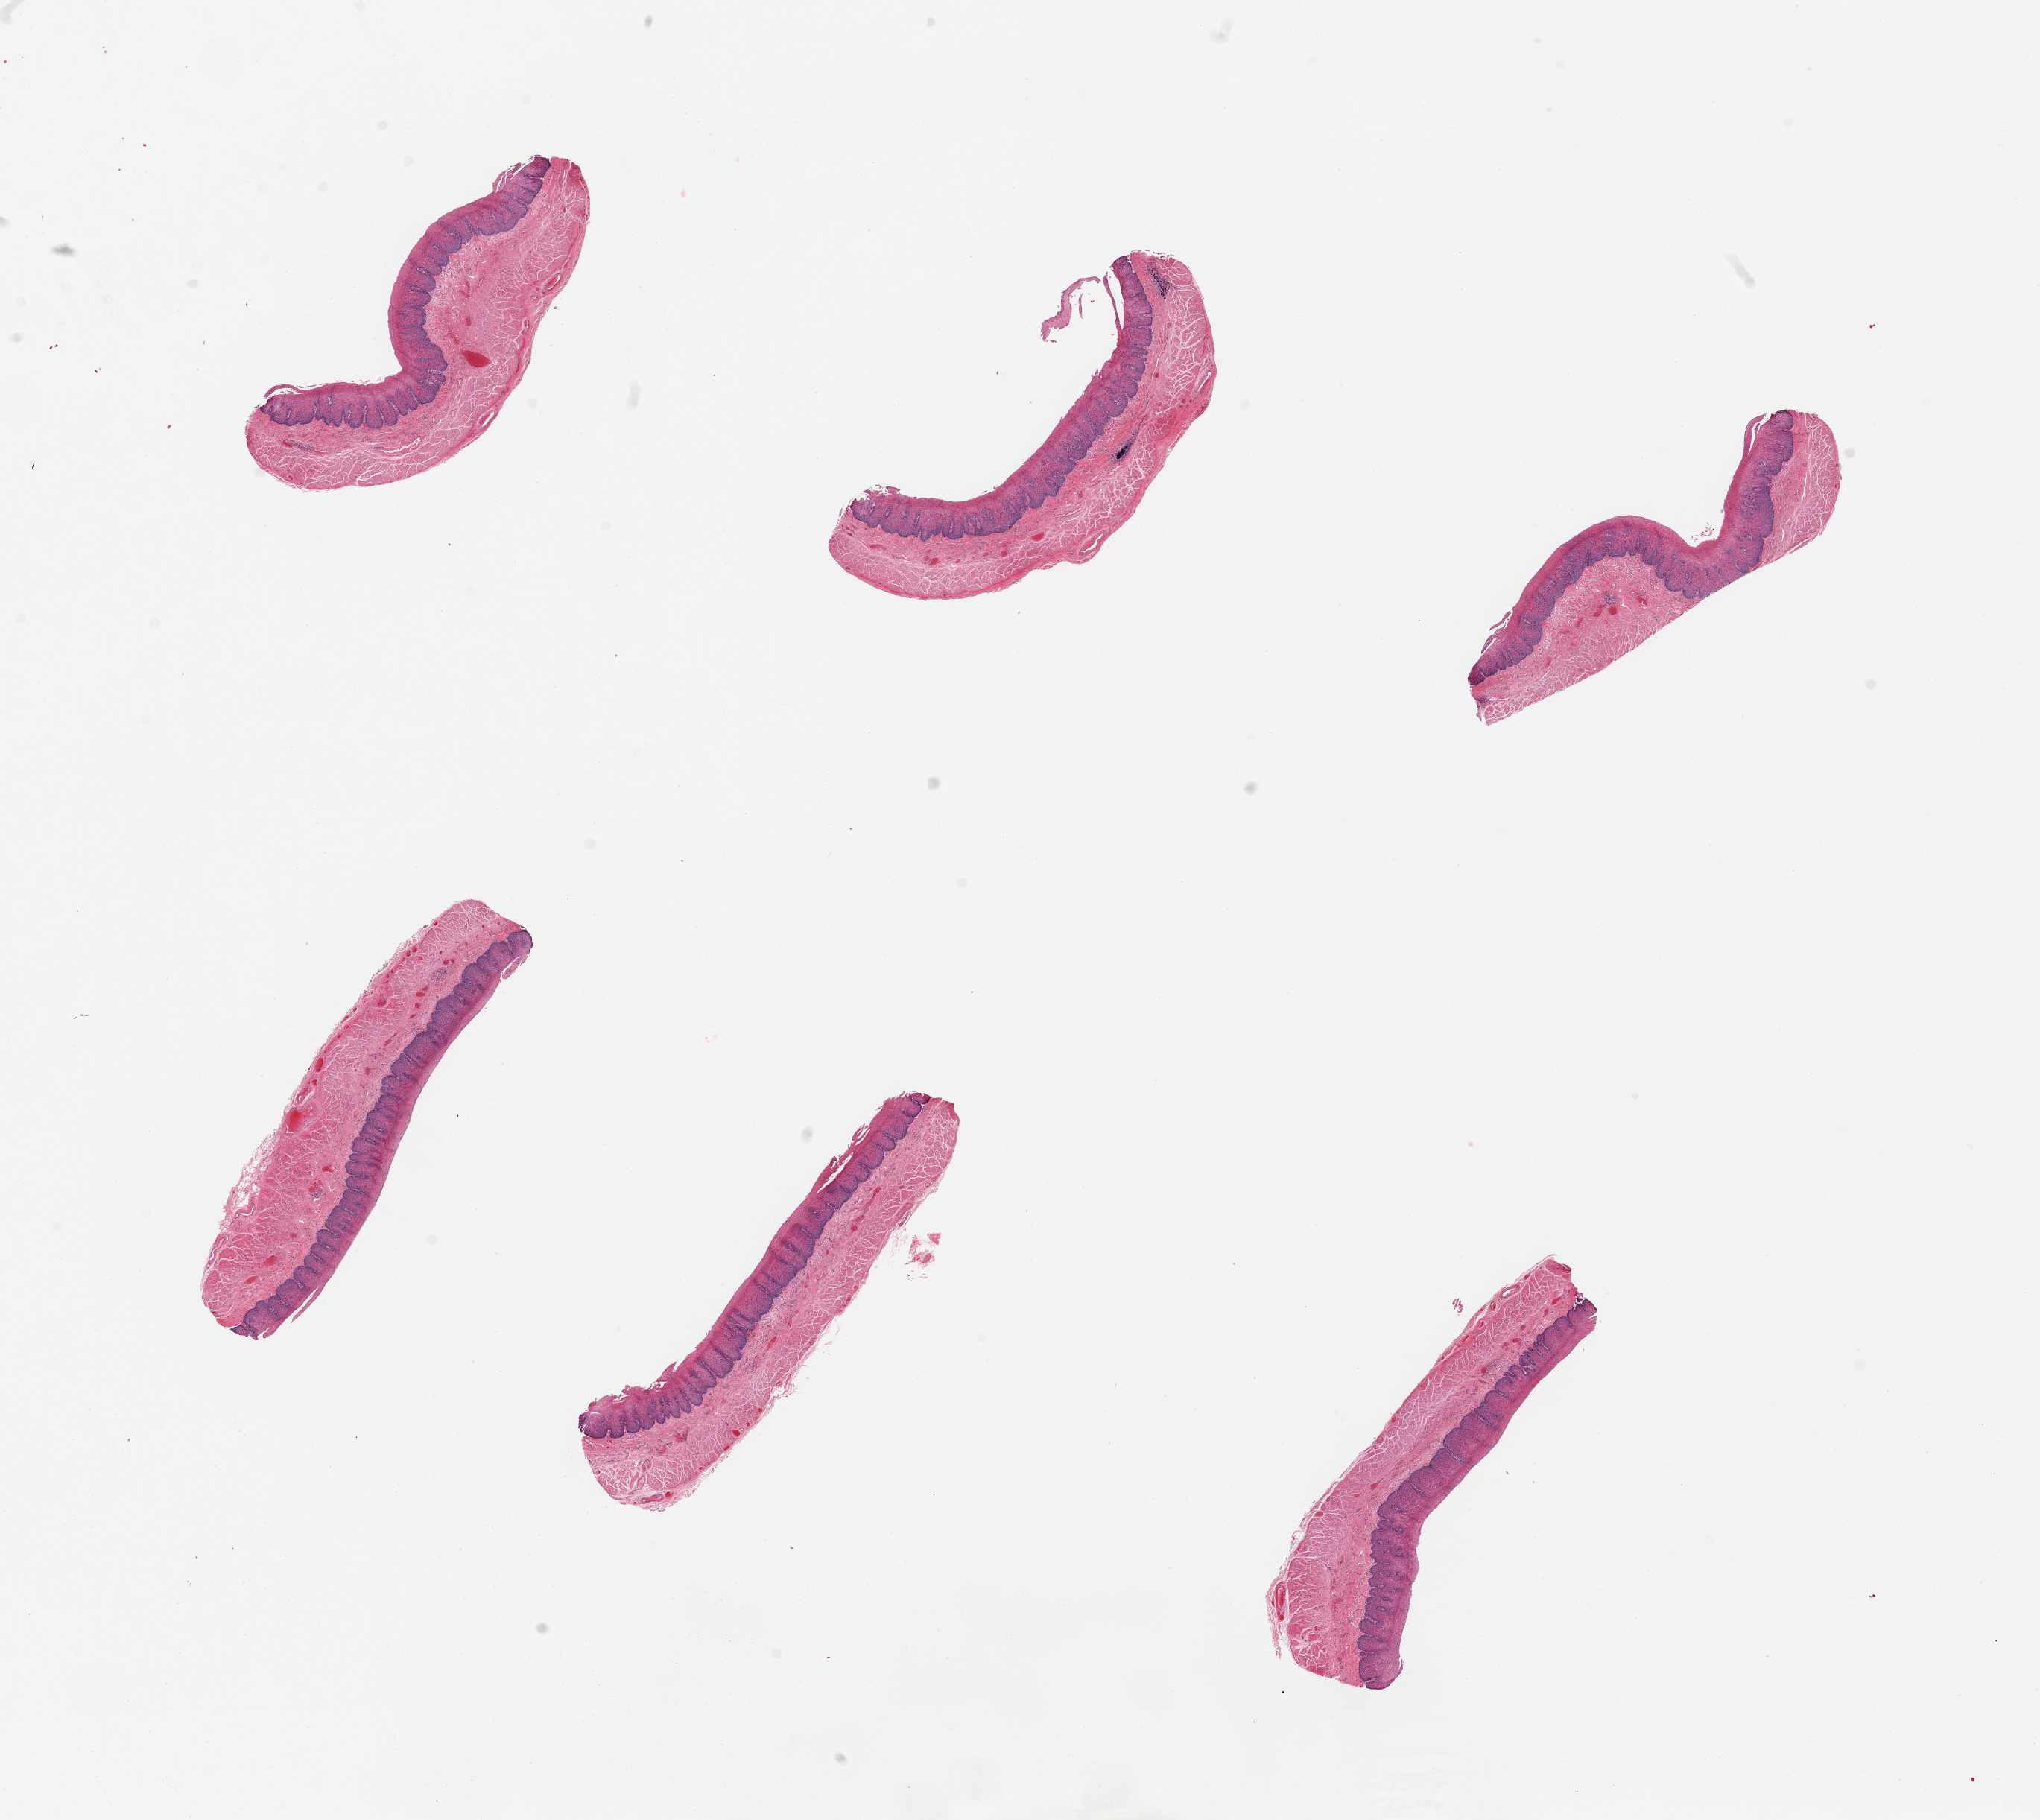
Digitized haematoxylin and eosin-stained section, low-resolution overview of the scanned area, about 21.7 x 19.3 mm (slide scanned at 20x). PAXgene-fixed paraffin-embedded (PFPE) section. Sampled site (target tissue): esophageal mucous membrane. Donor tissue sample.
* reviewer comment on this tissue sample: 6 pieces squamous mucosa is 0.3-0.4mm, ~30% thickness